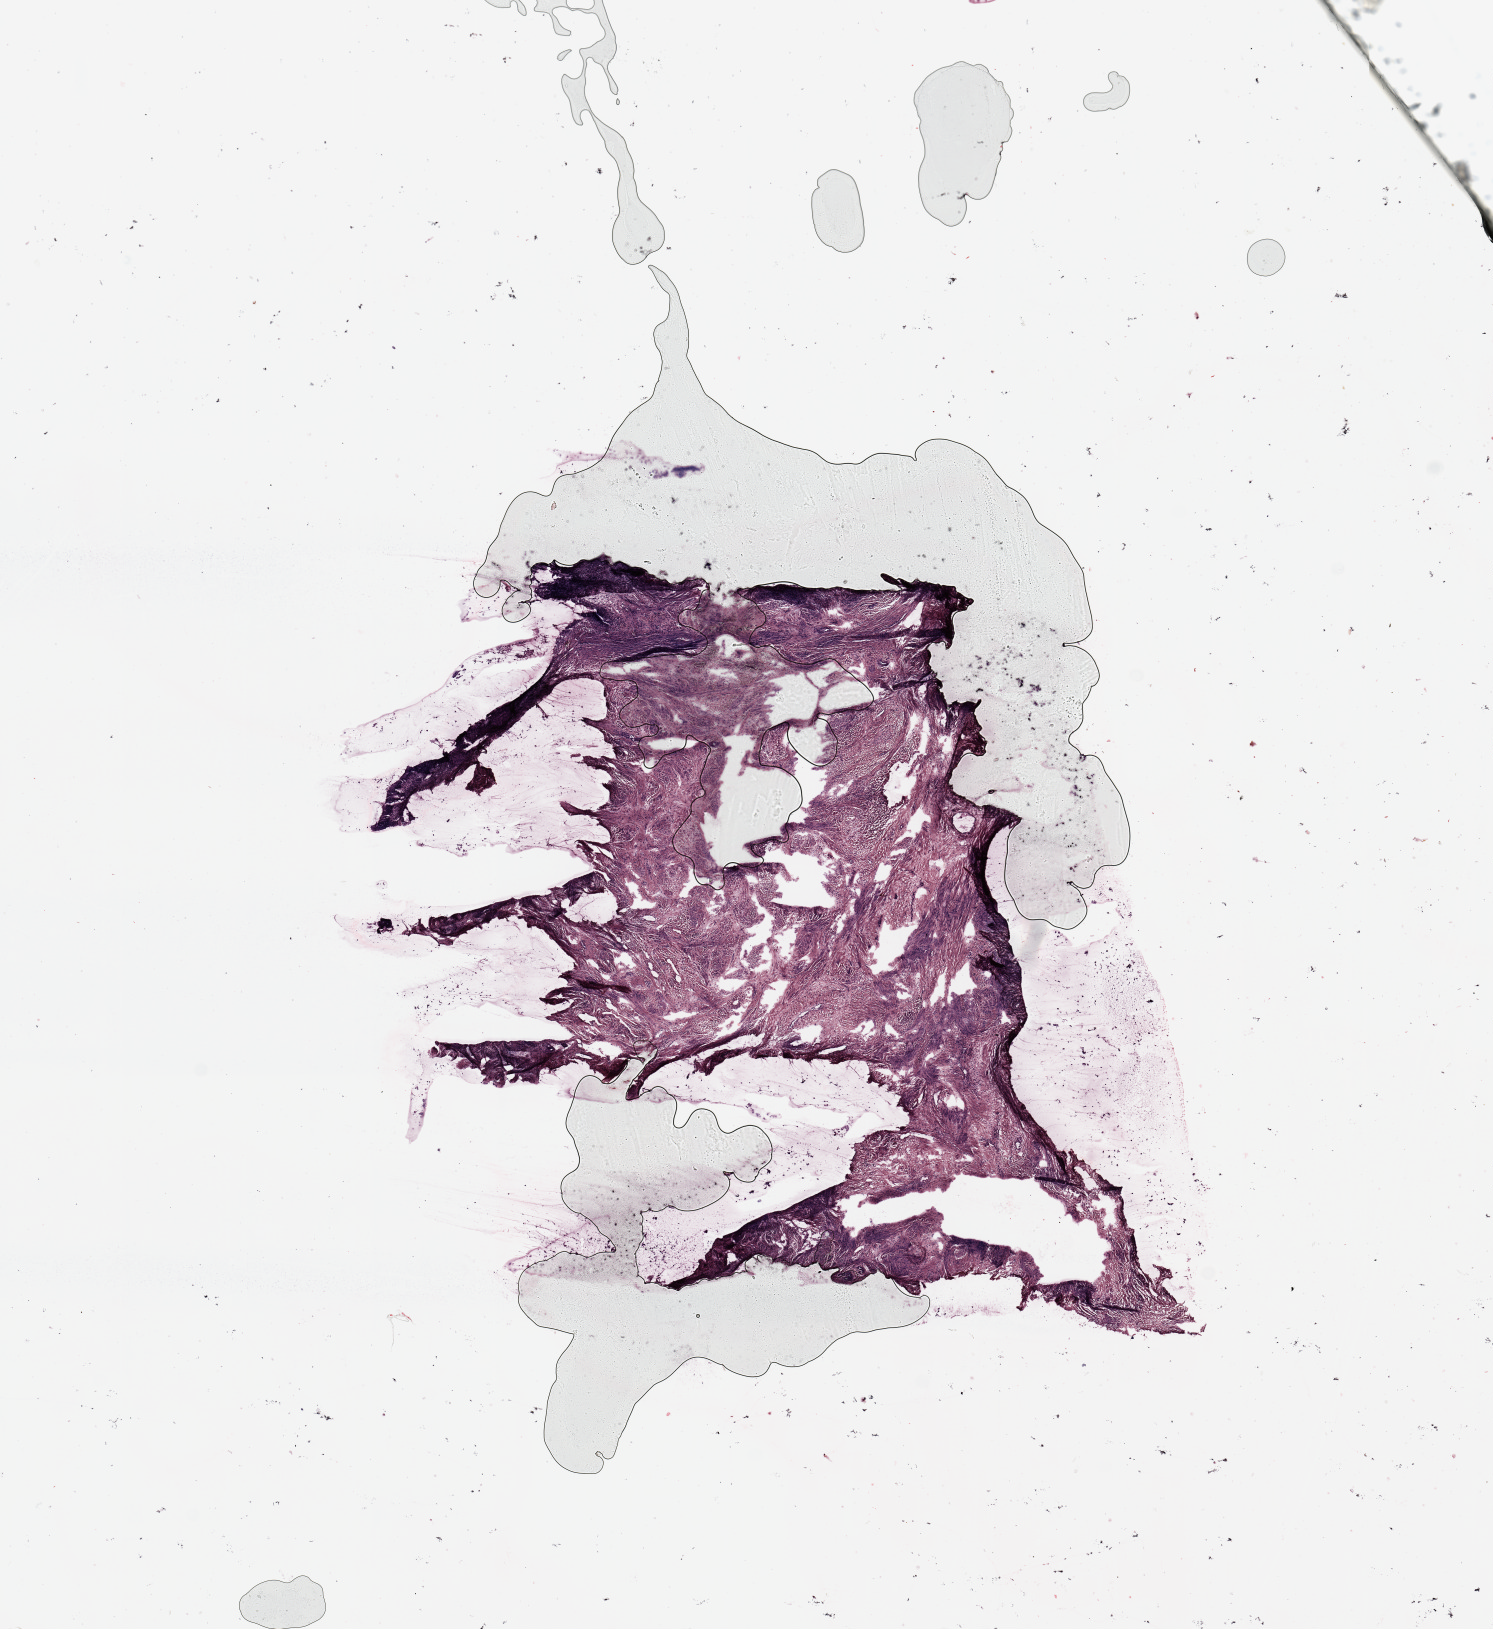
Whole-slide histology image, Hematoxylin and eosin (H&E) stained, shown as a low-resolution overview of the whole scanned area (about 11.8 x 12.9 mm, acquisition: 20x scan). Uterus, normal (non-tumour) tissue. 62-year-old female patient.
This section: normal (non-tumour) tissue from the same patient. Patient diagnosis: Endometrioid adenocarcinoma, NOS.